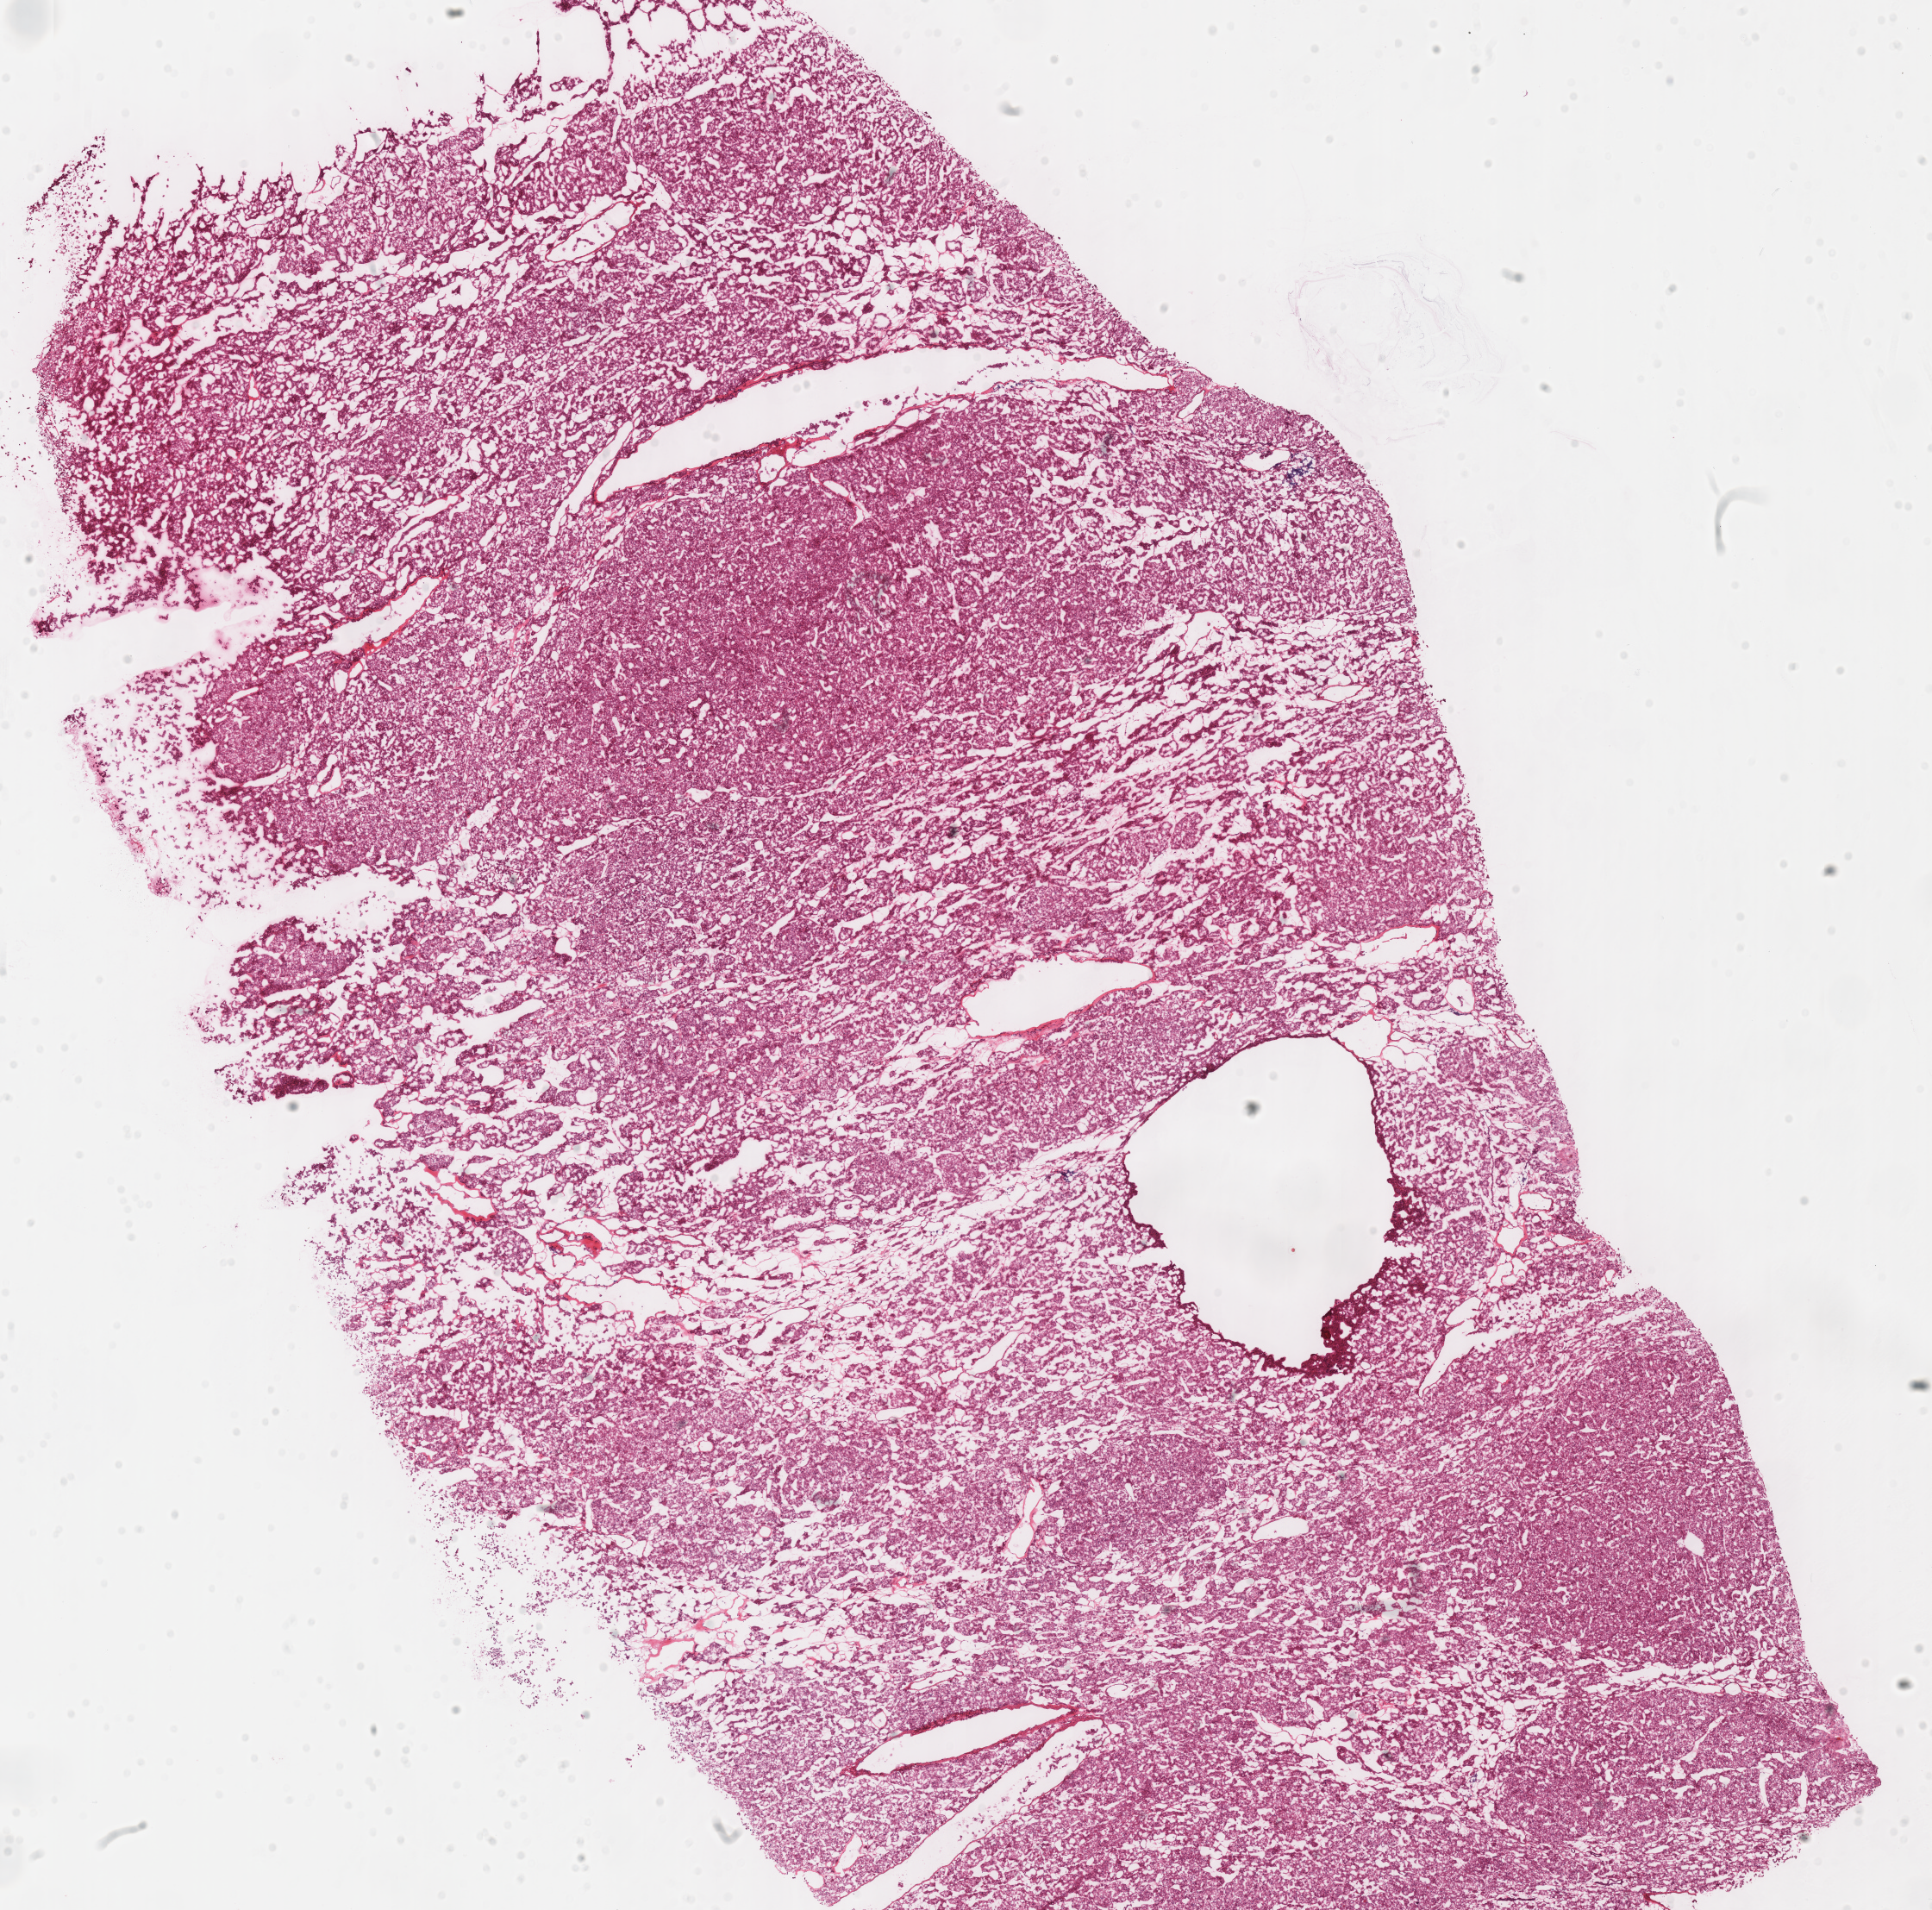
H&E-stained whole-slide image, whole scanned area (about 17.6 x 17.4 mm, slide scanned at 40x) shown as a low-resolution overview, frozen section from the top of the tissue portion, primary tumour sample from the kidney. Patient: male, age at initial diagnosis 69 years. Slide review estimates, as recorded: tumour cells 100%, tumour nuclei 90%, normal cells 0%, stromal cells 0%, necrosis 0%. Inflammatory infiltration, as recorded: lymphocyte infiltration 3%, monocyte infiltration 0%, neutrophil infiltration 0%.
Diagnosis: Renal cell carcinoma, chromophobe type. Laterality: right. Lymph nodes positive (case pathology): 0 of 14 examined. AJCC pathologic stage: III (5th edition).